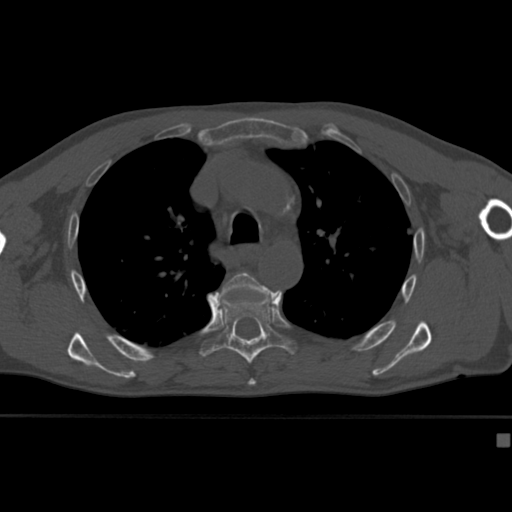
CT including the spine, one axial slice; position 298 of 430 along the scan axis; reconstruction kernel Br40s; bone window (W 1800 / L 400 HU); 1.5 mm slice thickness; 512 × 512 image matrix. Male patient, age 64 years. Case-level facts recorded for this patient, not image findings: primary cancer: uterus.
Annotated regions visible in this slice (semi-automatically segmented with operator editing):
- T5 vertebra: bounding box <215,272,281,382> (left, top, right, bottom; pixels)
- T6 vertebra: <199,291,297,364>